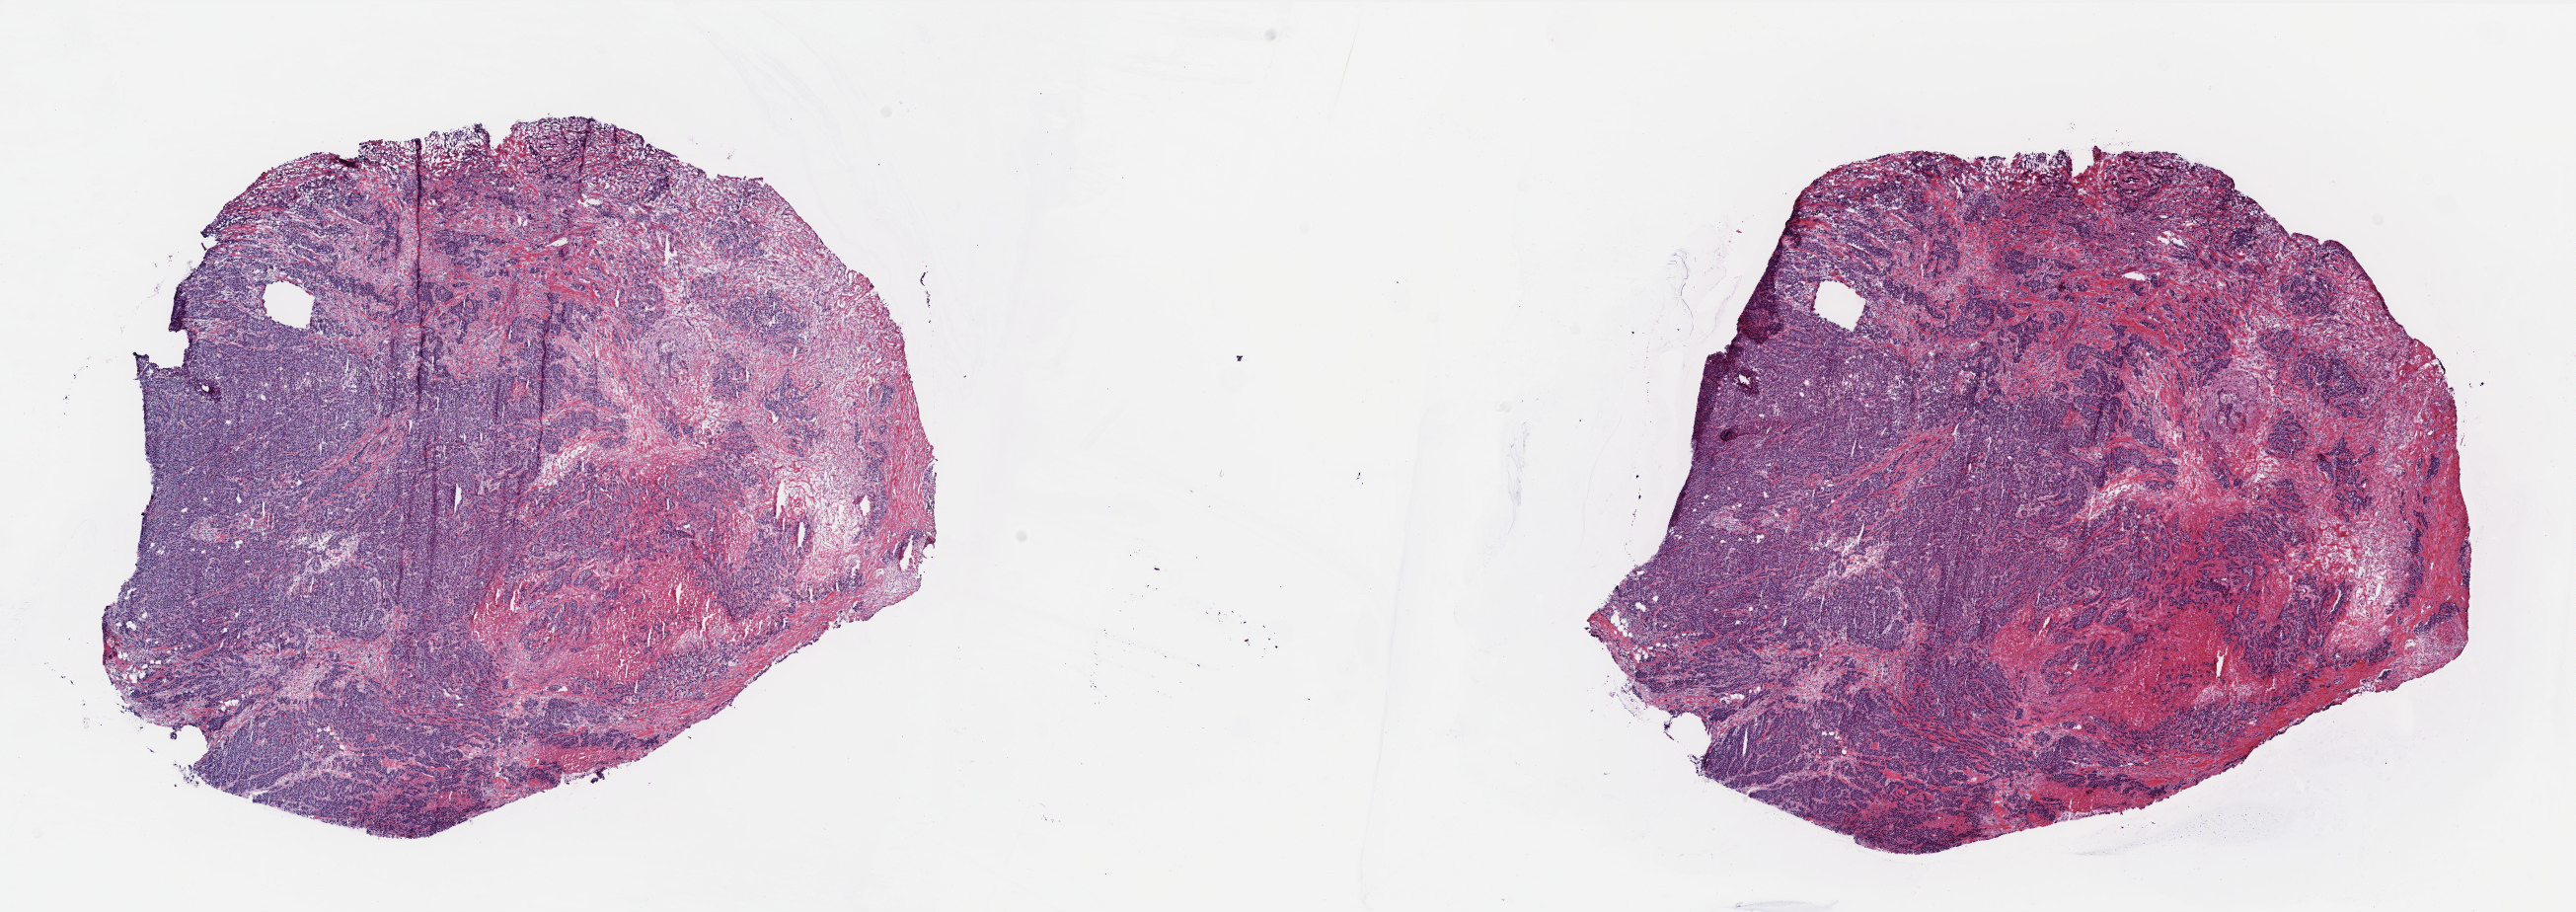
Whole-slide histology image, H&E, a low-resolution overview of the entire scanned area, about 20.9 x 7.4 mm (slide scanned at 40x). Frozen section. Breast, primary tumour sample. Patient: female, age at initial diagnosis 57 years. Slide review estimates, as recorded: tumour cells 78%, tumour nuclei 75%, normal cells 0%, stromal cells 17%, necrosis 5%. Infiltration values recorded for this section: lymphocyte infiltration 11%, monocyte infiltration 0%, neutrophil infiltration 0%.
• laterality: left
• histologic diagnosis: Infiltrating duct carcinoma, NOS
• lymph nodes positive (case pathology): 0 of 1 examined
• AJCC pathologic stage: IIA